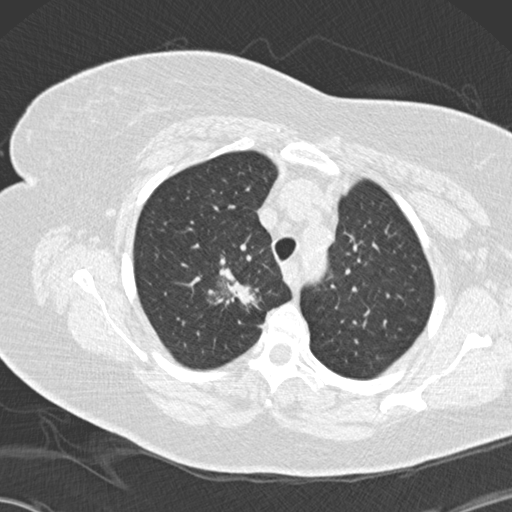
Low-dose screening chest CT, one axial slice; position 114 of 146 along the scan axis; reconstruction kernel B30f; 120 kVp; lung window (W 1500 / L -600 HU); 2 mm slice thickness; 512 × 512 image matrix, field of view 350 × 350 mm.
Outlined on this slice (expert manual segmentation):
- lesion 1 (tumor, upper lobe of right lung): box from (x=216, y=268) to (x=256, y=305) px